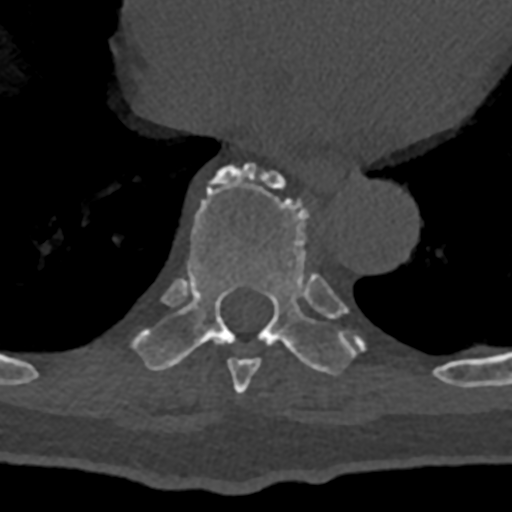
CT including the spine, one axial slice. Slice 671 of 797 in the series (ordered by position). Reconstruction kernel Br40s/3. 120 kVp. Bone window (W 1800 / L 400 HU). 0.5 mm slice thickness. 512 × 512 image matrix, field of view 160 × 160 mm. Patient: male, 74 years. From the clinical record (not read from this slice): primary cancer: renal; vertebrae with lytic lesions (as recorded): T10, L1, L2, L3, L4, L5.
Structures marked on this image (semi-automatic segmentation, software-assisted and operator-edited):
- T8 vertebra: bounding box <227,358,261,394> (left, top, right, bottom; pixels)
- T9 vertebra: <131,165,364,376>